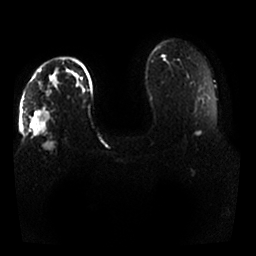
Breast MRI, one axial slice. Position 21 of 25 along the scan axis. Diffusion-weighted series; image 2 of 4 stored at this slice position (different b-values; order by instance number). 1.5 T. 256 × 256 image matrix, field of view 350 × 350 mm. Female patient.
Structures marked on this image (outlined manually by an expert reader):
- tumour on diffusion-weighted imaging: box from (x=32, y=76) to (x=58, y=152) px